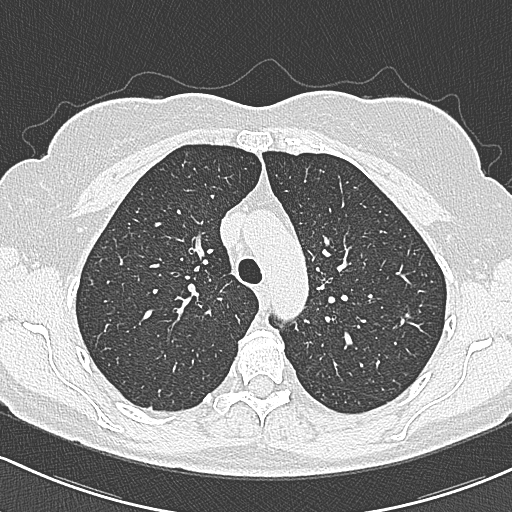
Axial slice from a low-dose chest CT screening exam, first (baseline) screen, lung window (W 1500 / L -600 HU), 1 mm slice thickness, slice 83 of 312 in the series, 512 × 512 image matrix. Female participant, aged 65 years at enrolment. Current smoker at enrolment.
Expert reader's lesion annotation, box from (x=377, y=297) to (x=422, y=339) px. The screening reader recorded 3 non-calcified nodules or masses ≥4 mm on this exam (left upper lobe, left upper lobe, right upper lobe); which of them this box marks is not recorded. Official screen result: positive, change unspecified: nodule(s) >= 4 mm or enlarging nodule(s), mass(es), or other non-specific abnormalities suspicious for lung cancer. Lung cancer was diagnosed 390 days after this screen: bronchiolo-alveolar carcinoma, non-mucinous, left upper lobe, stage IA (AJCC 6th edition), 10 mm at pathology.